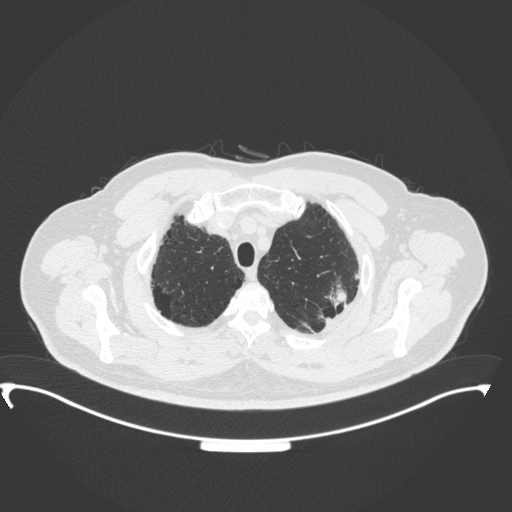
Chest CT, one axial slice. Slice 312 of 350 in the series (ordered by position). Reconstruction kernel B31f. 120 kVp. Lung window (W 1500 / L -600 HU). 1 mm slice thickness. 512 × 512 image matrix. Male patient, age 64 years. Case-level facts recorded for this patient, not image findings: clinical TNM (as recorded): T1c N1 M1.
Structures marked on this image (bounding box drawn by a radiologist):
- lung tumour (recorded histology: adenocarcinoma): bounding box [x1, y1, x2, y2] px = [323, 275, 351, 310]